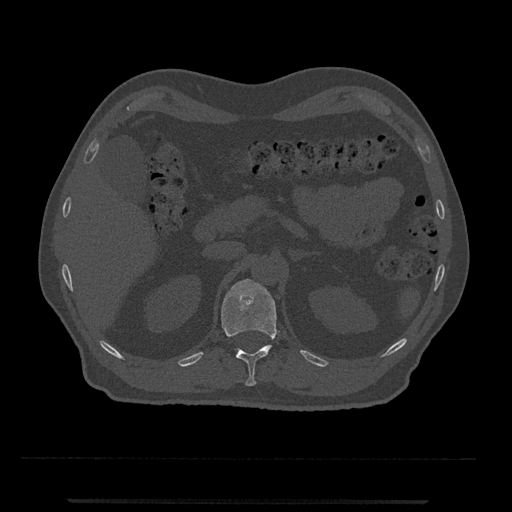
CT including the spine, one axial slice; position 391 of 797 along the scan axis; 120 kVp; bone window (W 1800 / L 400 HU); 512 × 512 image matrix. Patient: male, 63 years. From the clinical record (not read from this slice): primary cancer: prostate.
Structures marked on this image (semi-automatic segmentation, software-assisted and operator-edited):
- T12 vertebra: bounding box (x1, y1, x2, y2) in pixels: (221, 279, 278, 386)